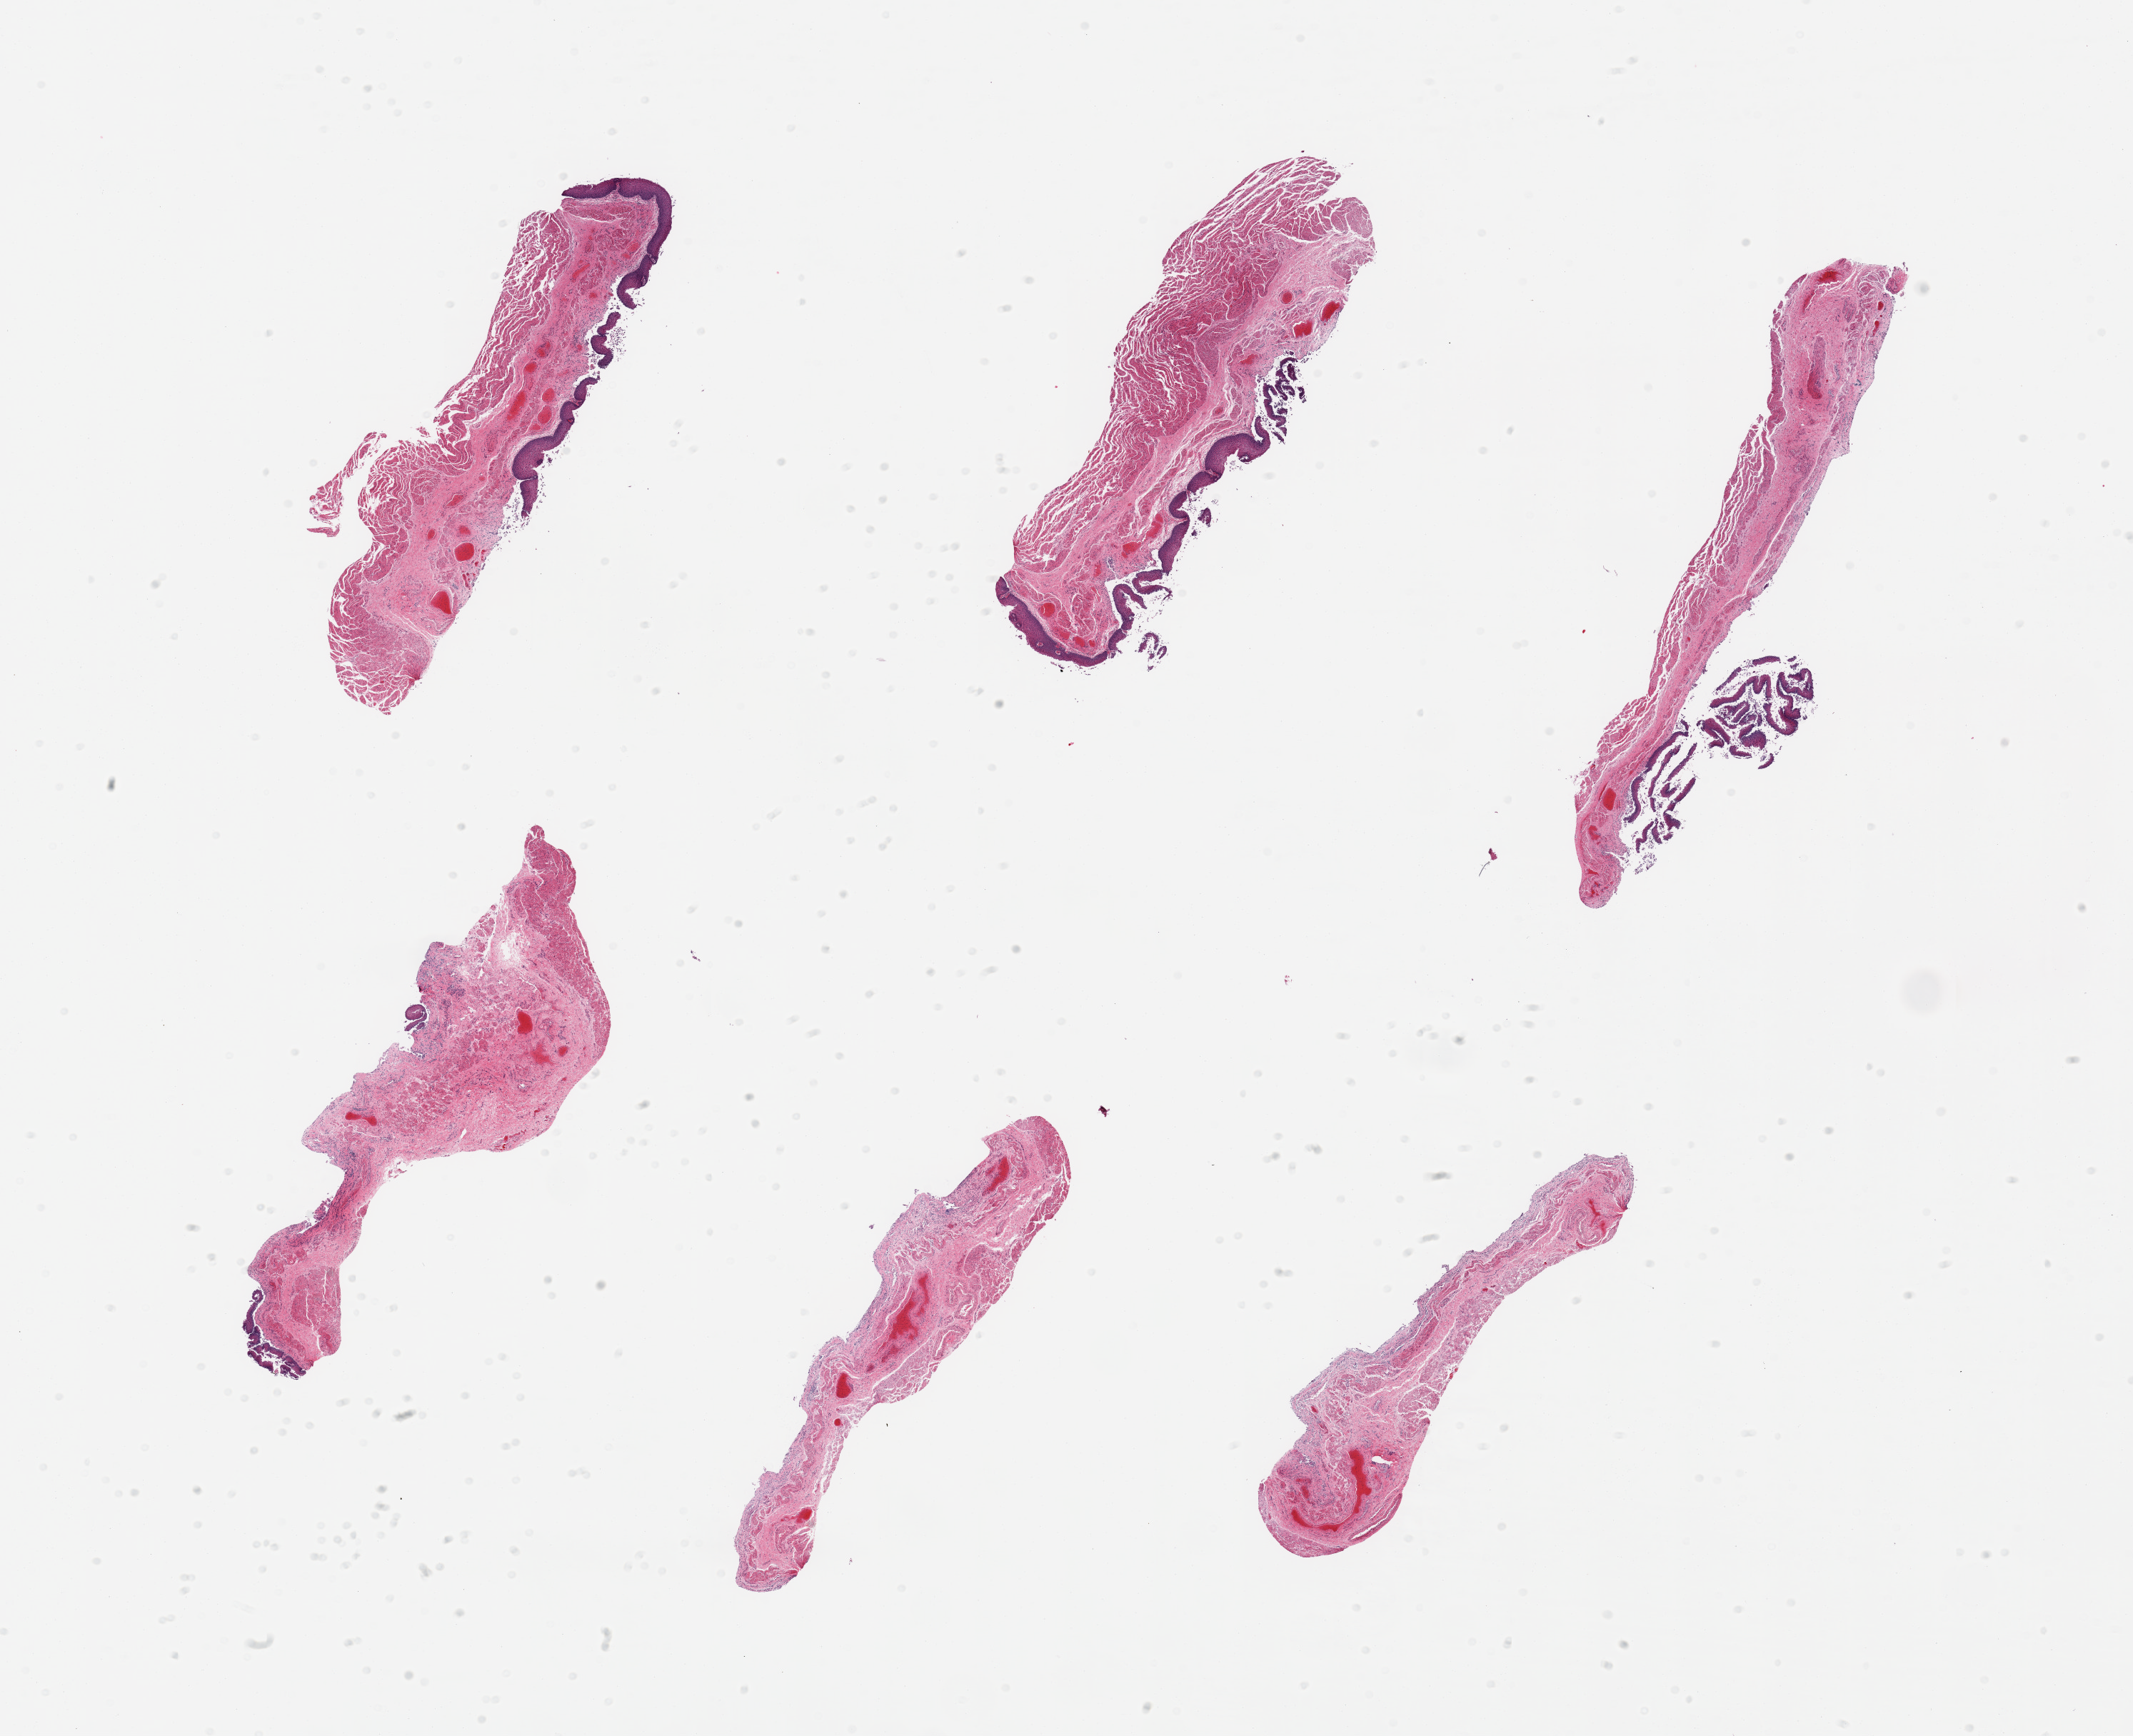
Haematoxylin and eosin whole-slide image, a low-resolution overview of the entire scanned area, about 23.6 x 19.2 mm. PAXgene-fixed, paraffin-embedded tissue. Sampled site (target tissue): esophageal mucous membrane. Donor tissue sample. Male donor.
* reviewer comment on this tissue sample: 6 pieces; epithelium sloughing/absent in some sections; muscularis (not target) also present